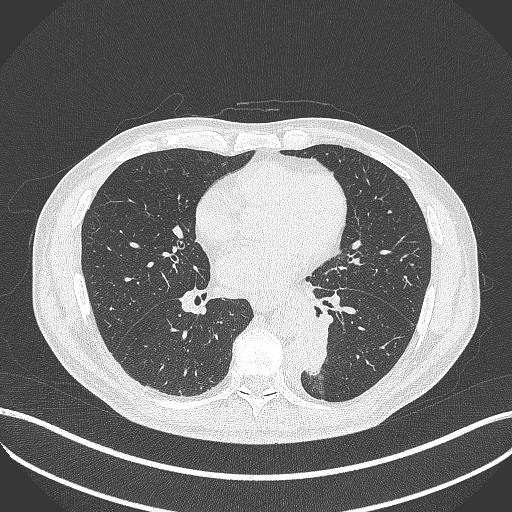
Chest CT, one axial slice; slice 189 of 451 in the series (ordered by position); reconstruction kernel B70f; 120 kVp; lung window (W 1500 / L -600 HU); 1 mm slice thickness; 512 × 512 image matrix, field of view 400 × 400 mm. Patient: male, 72 years. Case-level facts recorded for this patient, not image findings: clinical TNM (as recorded): T2b N0 M1.
Structures marked on this image (bounding box drawn by a radiologist):
- lung tumour (recorded histology: adenocarcinoma): bounding box (x1, y1, x2, y2) in pixels: (298, 324, 334, 377)